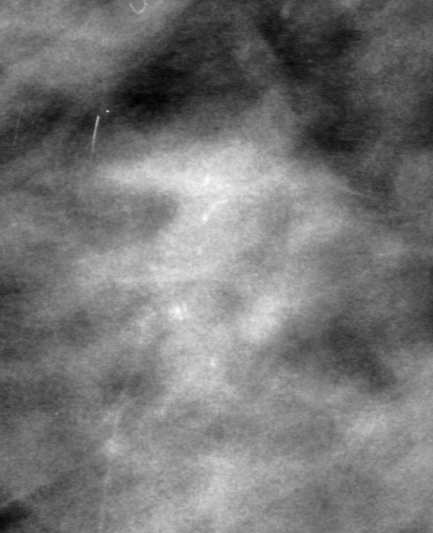
Region of interest cut from a scanned film mammogram (one marked finding), left breast, CC view, BI-RADS breast density category 3 (scale 1–4).
Finding: calcifications, morphology amorphous, distribution clustered; BI-RADS assessment category 0 (incomplete: needs additional imaging); pathology result (as recorded, not read from the image): benign.